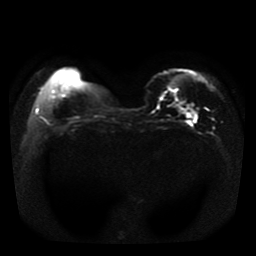
Breast MRI, one axial slice. Position 10 of 41 along the scan axis. Diffusion-weighted series; image 2 of 4 stored at this slice position (different b-values; order by instance number). 1.5 T. 256 × 256 image matrix. Female patient.
Outlined on this slice (manually delineated by an expert):
- tumour on diffusion-weighted imaging: box from (x=180, y=108) to (x=197, y=120) px